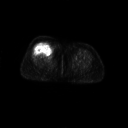
FDG PET of an extremity soft-tissue mass (from a PET/CT study), one axial slice; position 30 of 267 along the scan axis; 3.27 mm slice thickness; 128 × 128 image matrix, field of view 700 × 700 mm. Female patient, age 56 years. Case-level facts recorded for this patient, not image findings: histological type: malignant solitary fibrous tumor; grade: intermediate; site of the primary tumour: right thigh.
Structures marked on this image (expert contour drawn on MRI and transferred to this co-registered scan by the dataset authors):
- gross tumour volume including surrounding oedema: bounding box [x1, y1, x2, y2] px = [35, 41, 55, 58]
- gross tumour volume (mass): [36, 41, 54, 57]